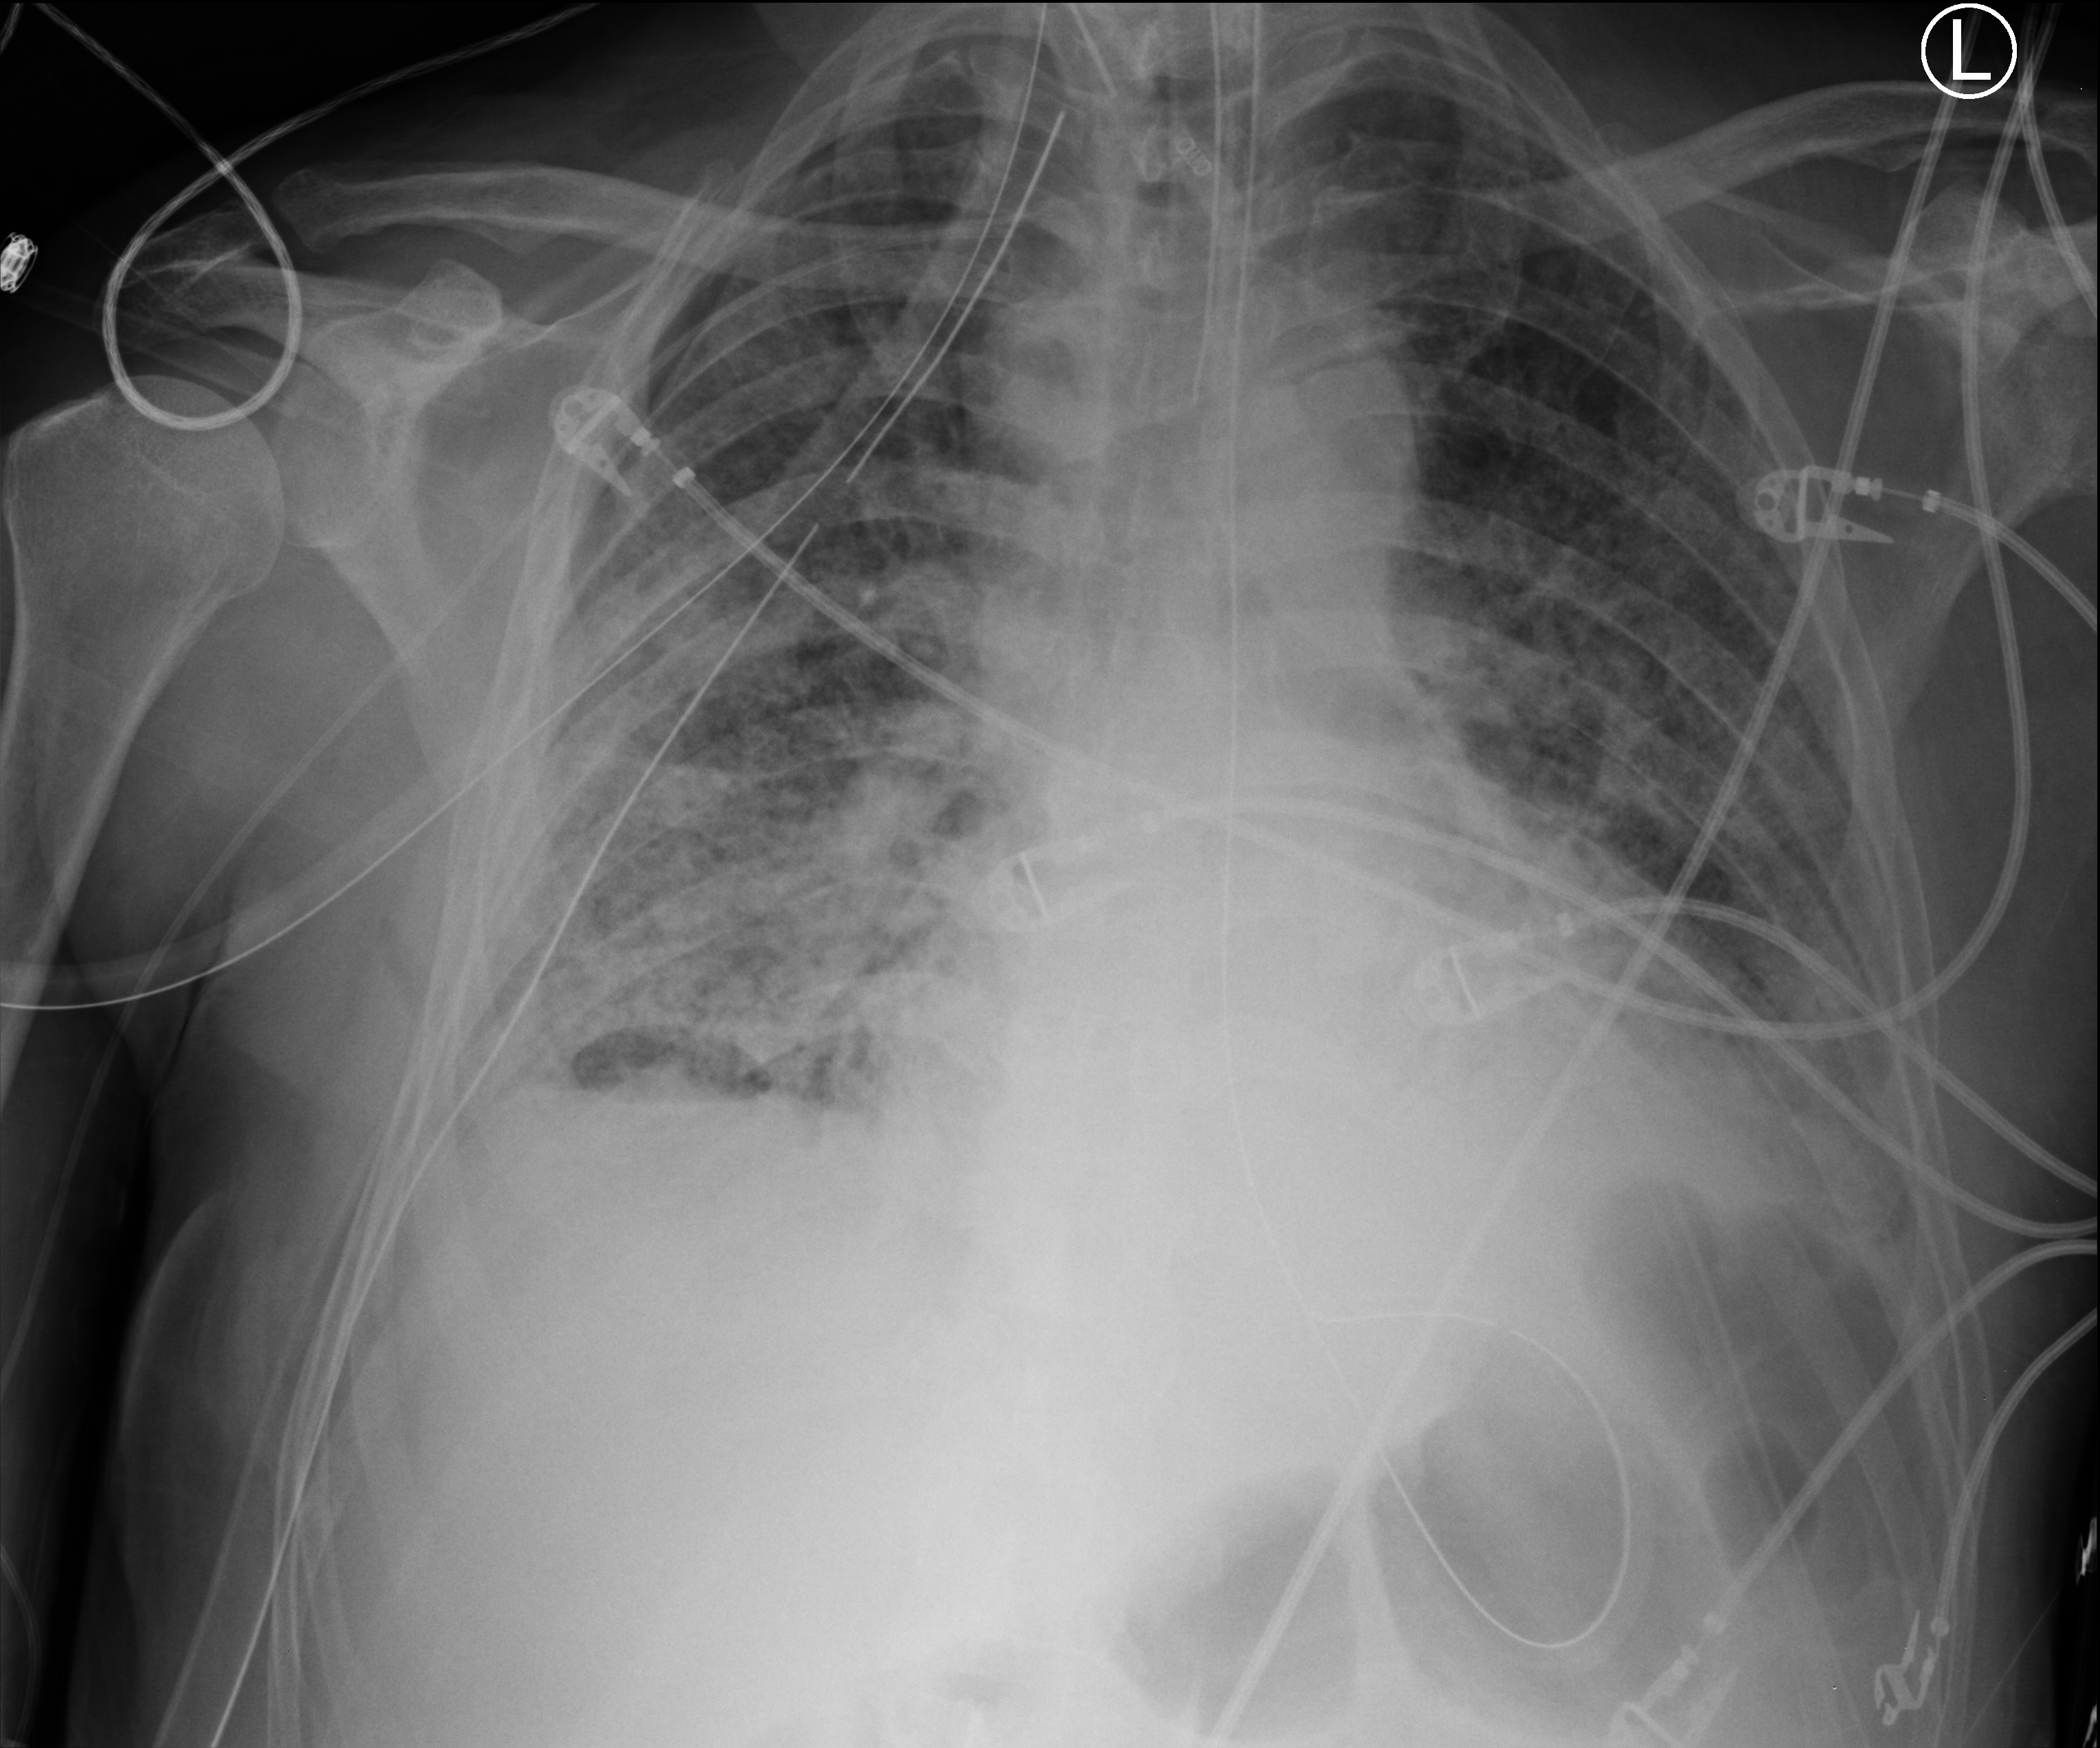
Chest X-ray (portable), anteroposterior (AP) projection. Male patient hospitalised with COVID-19, age 60–74 years.
From the hospital-stay record, not from the radiograph (when in the stay this image was taken is not recorded):
- mechanically ventilated during this hospital stay: yes
- length of hospital stay: 37 days